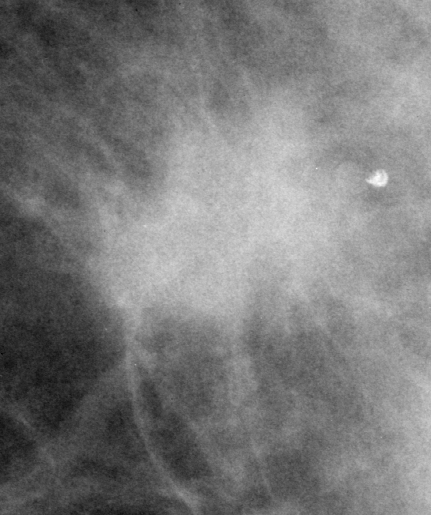
Cropped region of a digitized screen-film mammogram centred on a radiologist-marked abnormality, left breast, CC view.
Mass, shape irregular / architectural distortion, margins spiculated; BI-RADS assessment category 4; pathology (as recorded): malignant.